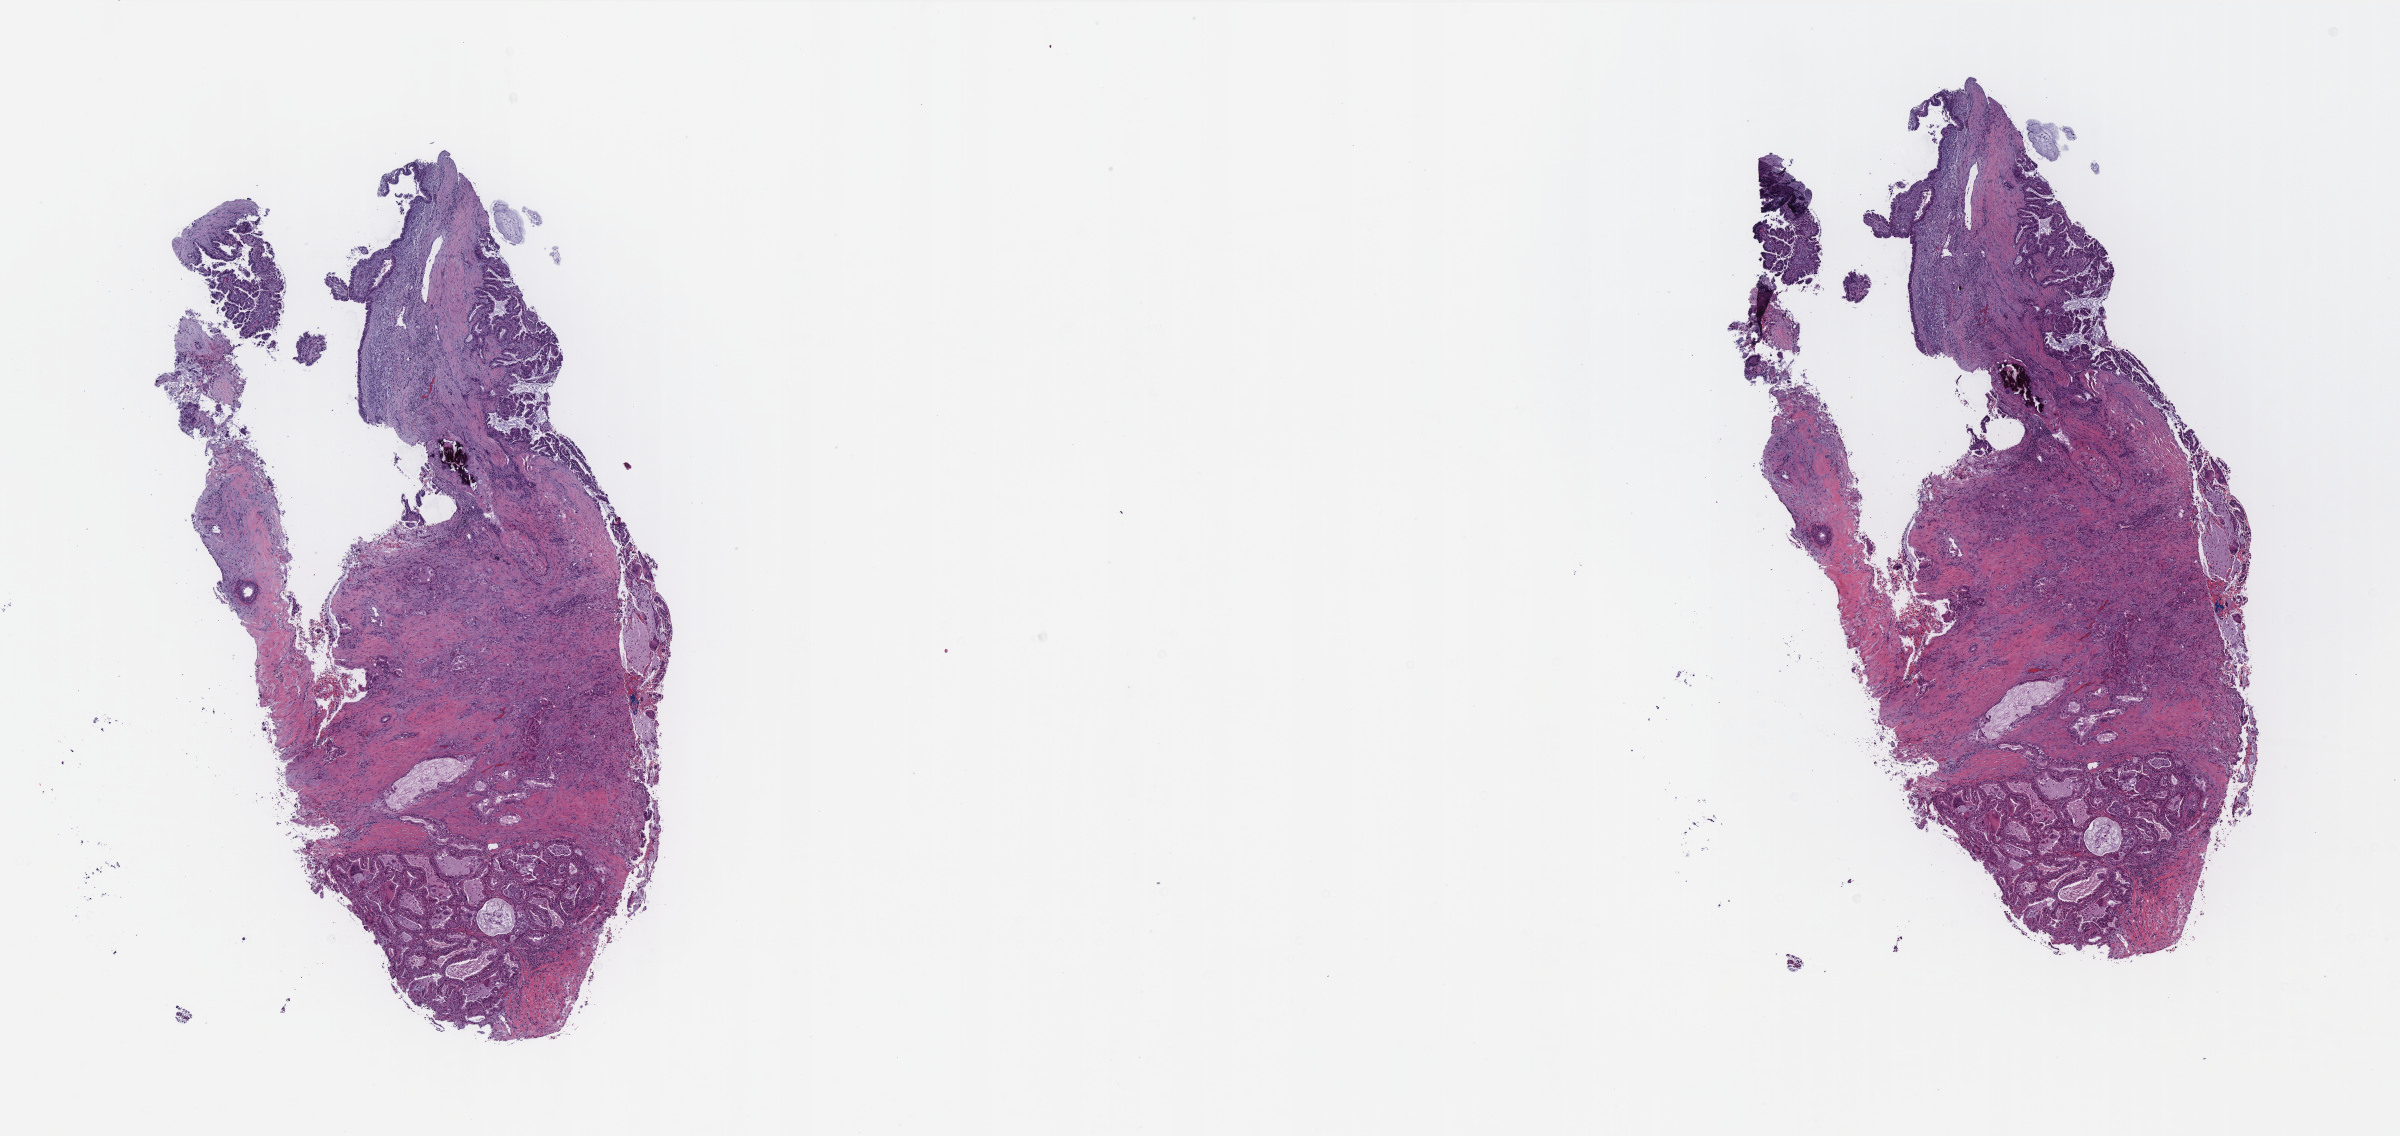
Whole-slide histology image, H&E, low-resolution overview of the scanned area, about 19.2 x 9.1 mm; formalin-fixed paraffin-embedded (FFPE) diagnostic section; lung, primary tumour sample. Male, age 74 years at initial diagnosis.
• AJCC pathologic stage: IIB (7th edition)
• diagnosis: Adenocarcinoma, NOS (upper lobe, lung)
• laterality: left